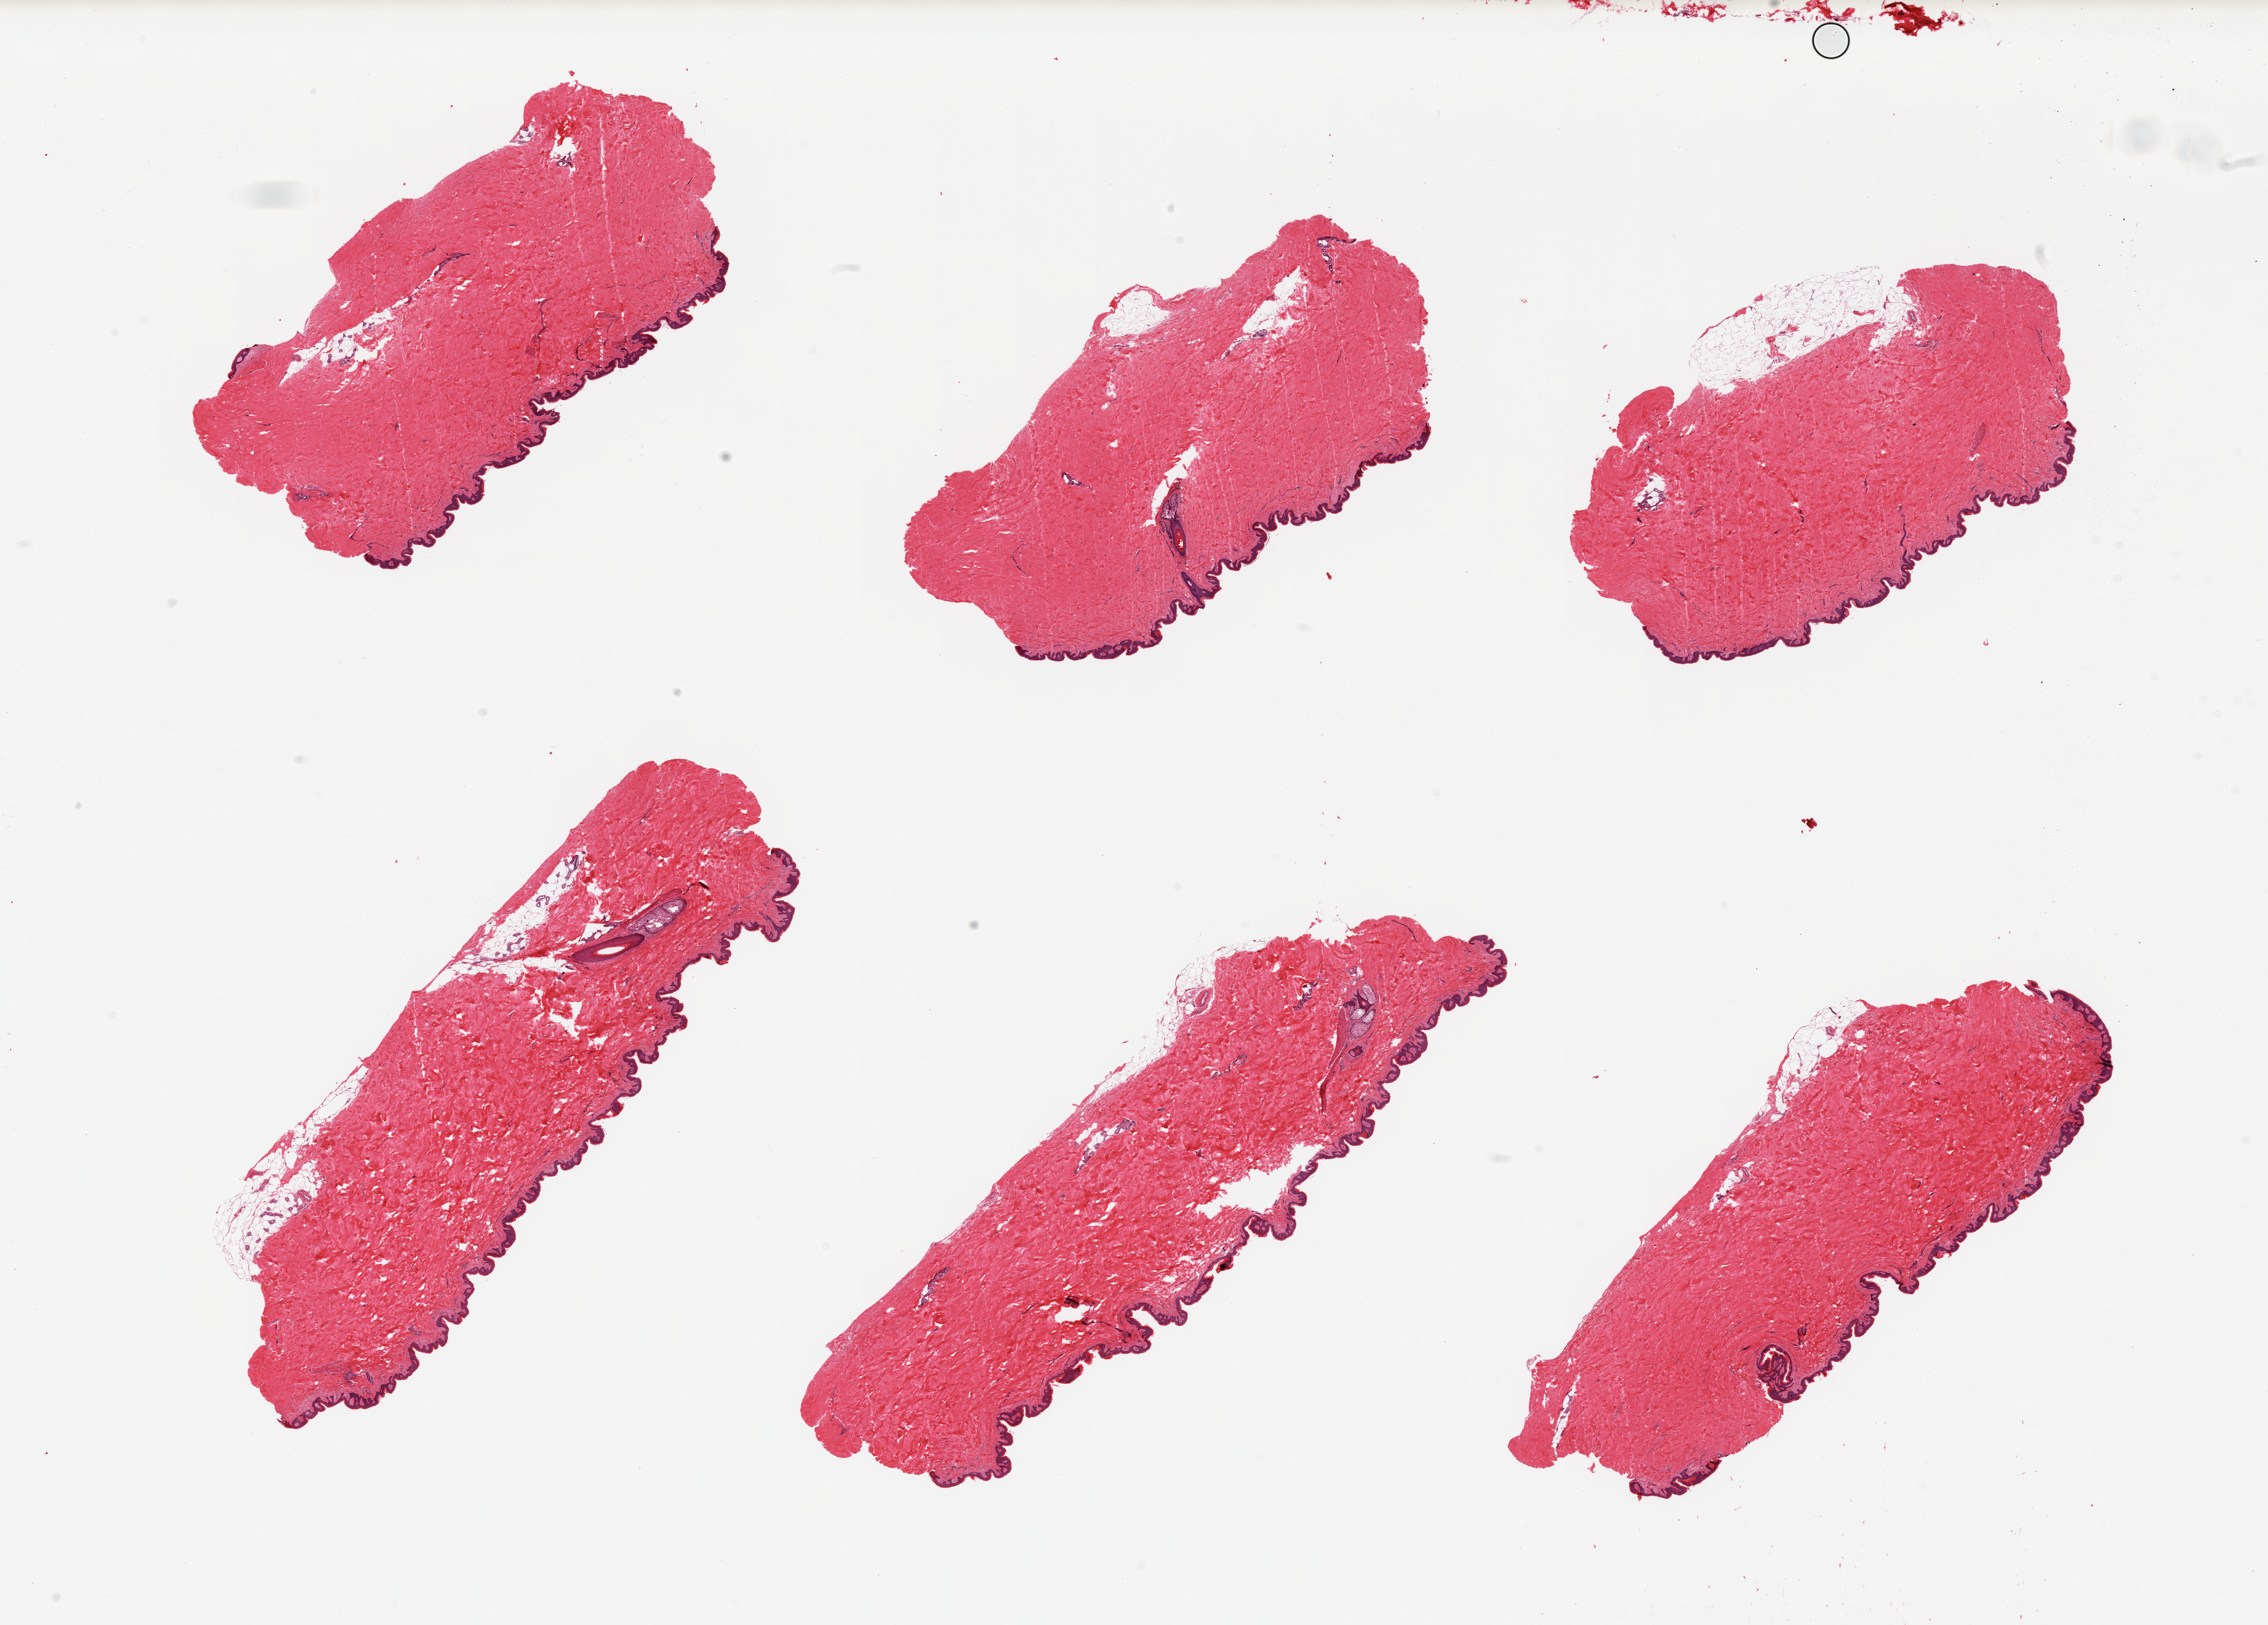
H&E whole-slide image, a low-resolution overview of the entire scanned area, about 28.5 x 20.5 mm, PAXgene-fixed, paraffin-embedded tissue, section of skin of suprapubic region (target tissue), donor tissue sample. Male donor.
Reviewer comment on this tissue sample: 6 pieces; generally well trimmed.